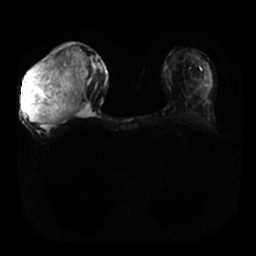
Breast MRI, one axial slice; diffusion-weighted series; image 2 of 4 stored at this slice position (different b-values; order by instance number); 1.5 T; 4 mm slice thickness; 256 × 256 image matrix, field of view 340 × 340 mm. Female patient.
Outlined on this slice (manually delineated by an expert):
- tumour on diffusion-weighted imaging: box from (x=22, y=50) to (x=88, y=124) px